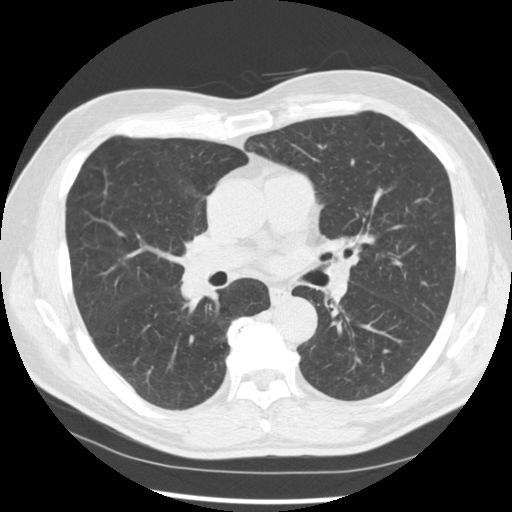
Low-dose screening chest CT, one axial slice; slice 156 of 277 in the series (ordered by position); lung window (W 1500 / L -600 HU); 2.5 mm slice thickness; 512 × 512 image matrix.
Annotated regions visible in this slice (manually delineated by an expert):
- lesion 1 (tumor, middle lobe of right lung): box from (x=180, y=264) to (x=209, y=302) px